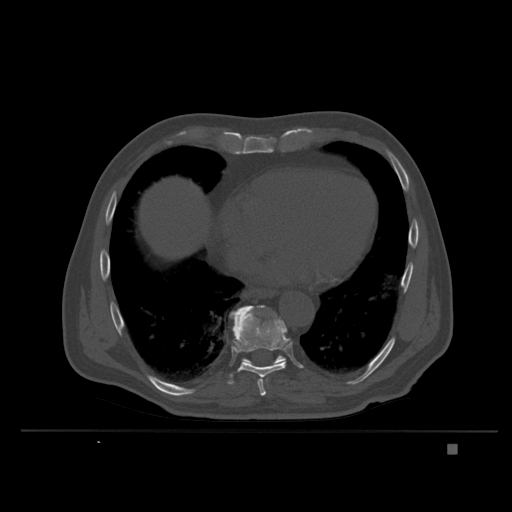
CT including the spine, one axial slice. Position 209 of 435 along the scan axis. Bone window (W 1800 / L 400 HU). 1.5 mm slice thickness. 512 × 512 image matrix, field of view 434 × 434 mm. Male patient, age 73 years. Case-level facts recorded for this patient, not image findings: primary cancer: skin.
Structures marked on this image (semi-automatic segmentation, software-assisted and operator-edited):
- T10 vertebra: bounding box (x1, y1, x2, y2) in pixels: (242, 355, 286, 366)
- T9 vertebra: (227, 305, 289, 396)